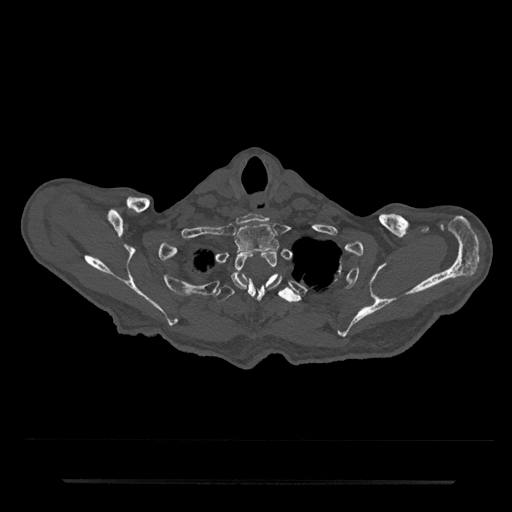
CT including the spine, one axial slice. Position 689 of 797 along the scan axis. Reconstruction kernel Br40s/3. Bone window (W 1800 / L 400 HU). 0.5 mm slice thickness. 512 × 512 image matrix, field of view 427 × 427 mm. Patient: male, 74 years. From the clinical record (not read from this slice): primary cancer: prostate.
Structures marked on this image (semi-automatic segmentation, software-assisted and operator-edited):
- T1 vertebra: box from (x=234, y=223) to (x=280, y=253) px
- T2 vertebra: (x=231, y=249)–(x=282, y=301)
- T3 vertebra: (x=214, y=273)–(x=301, y=303)